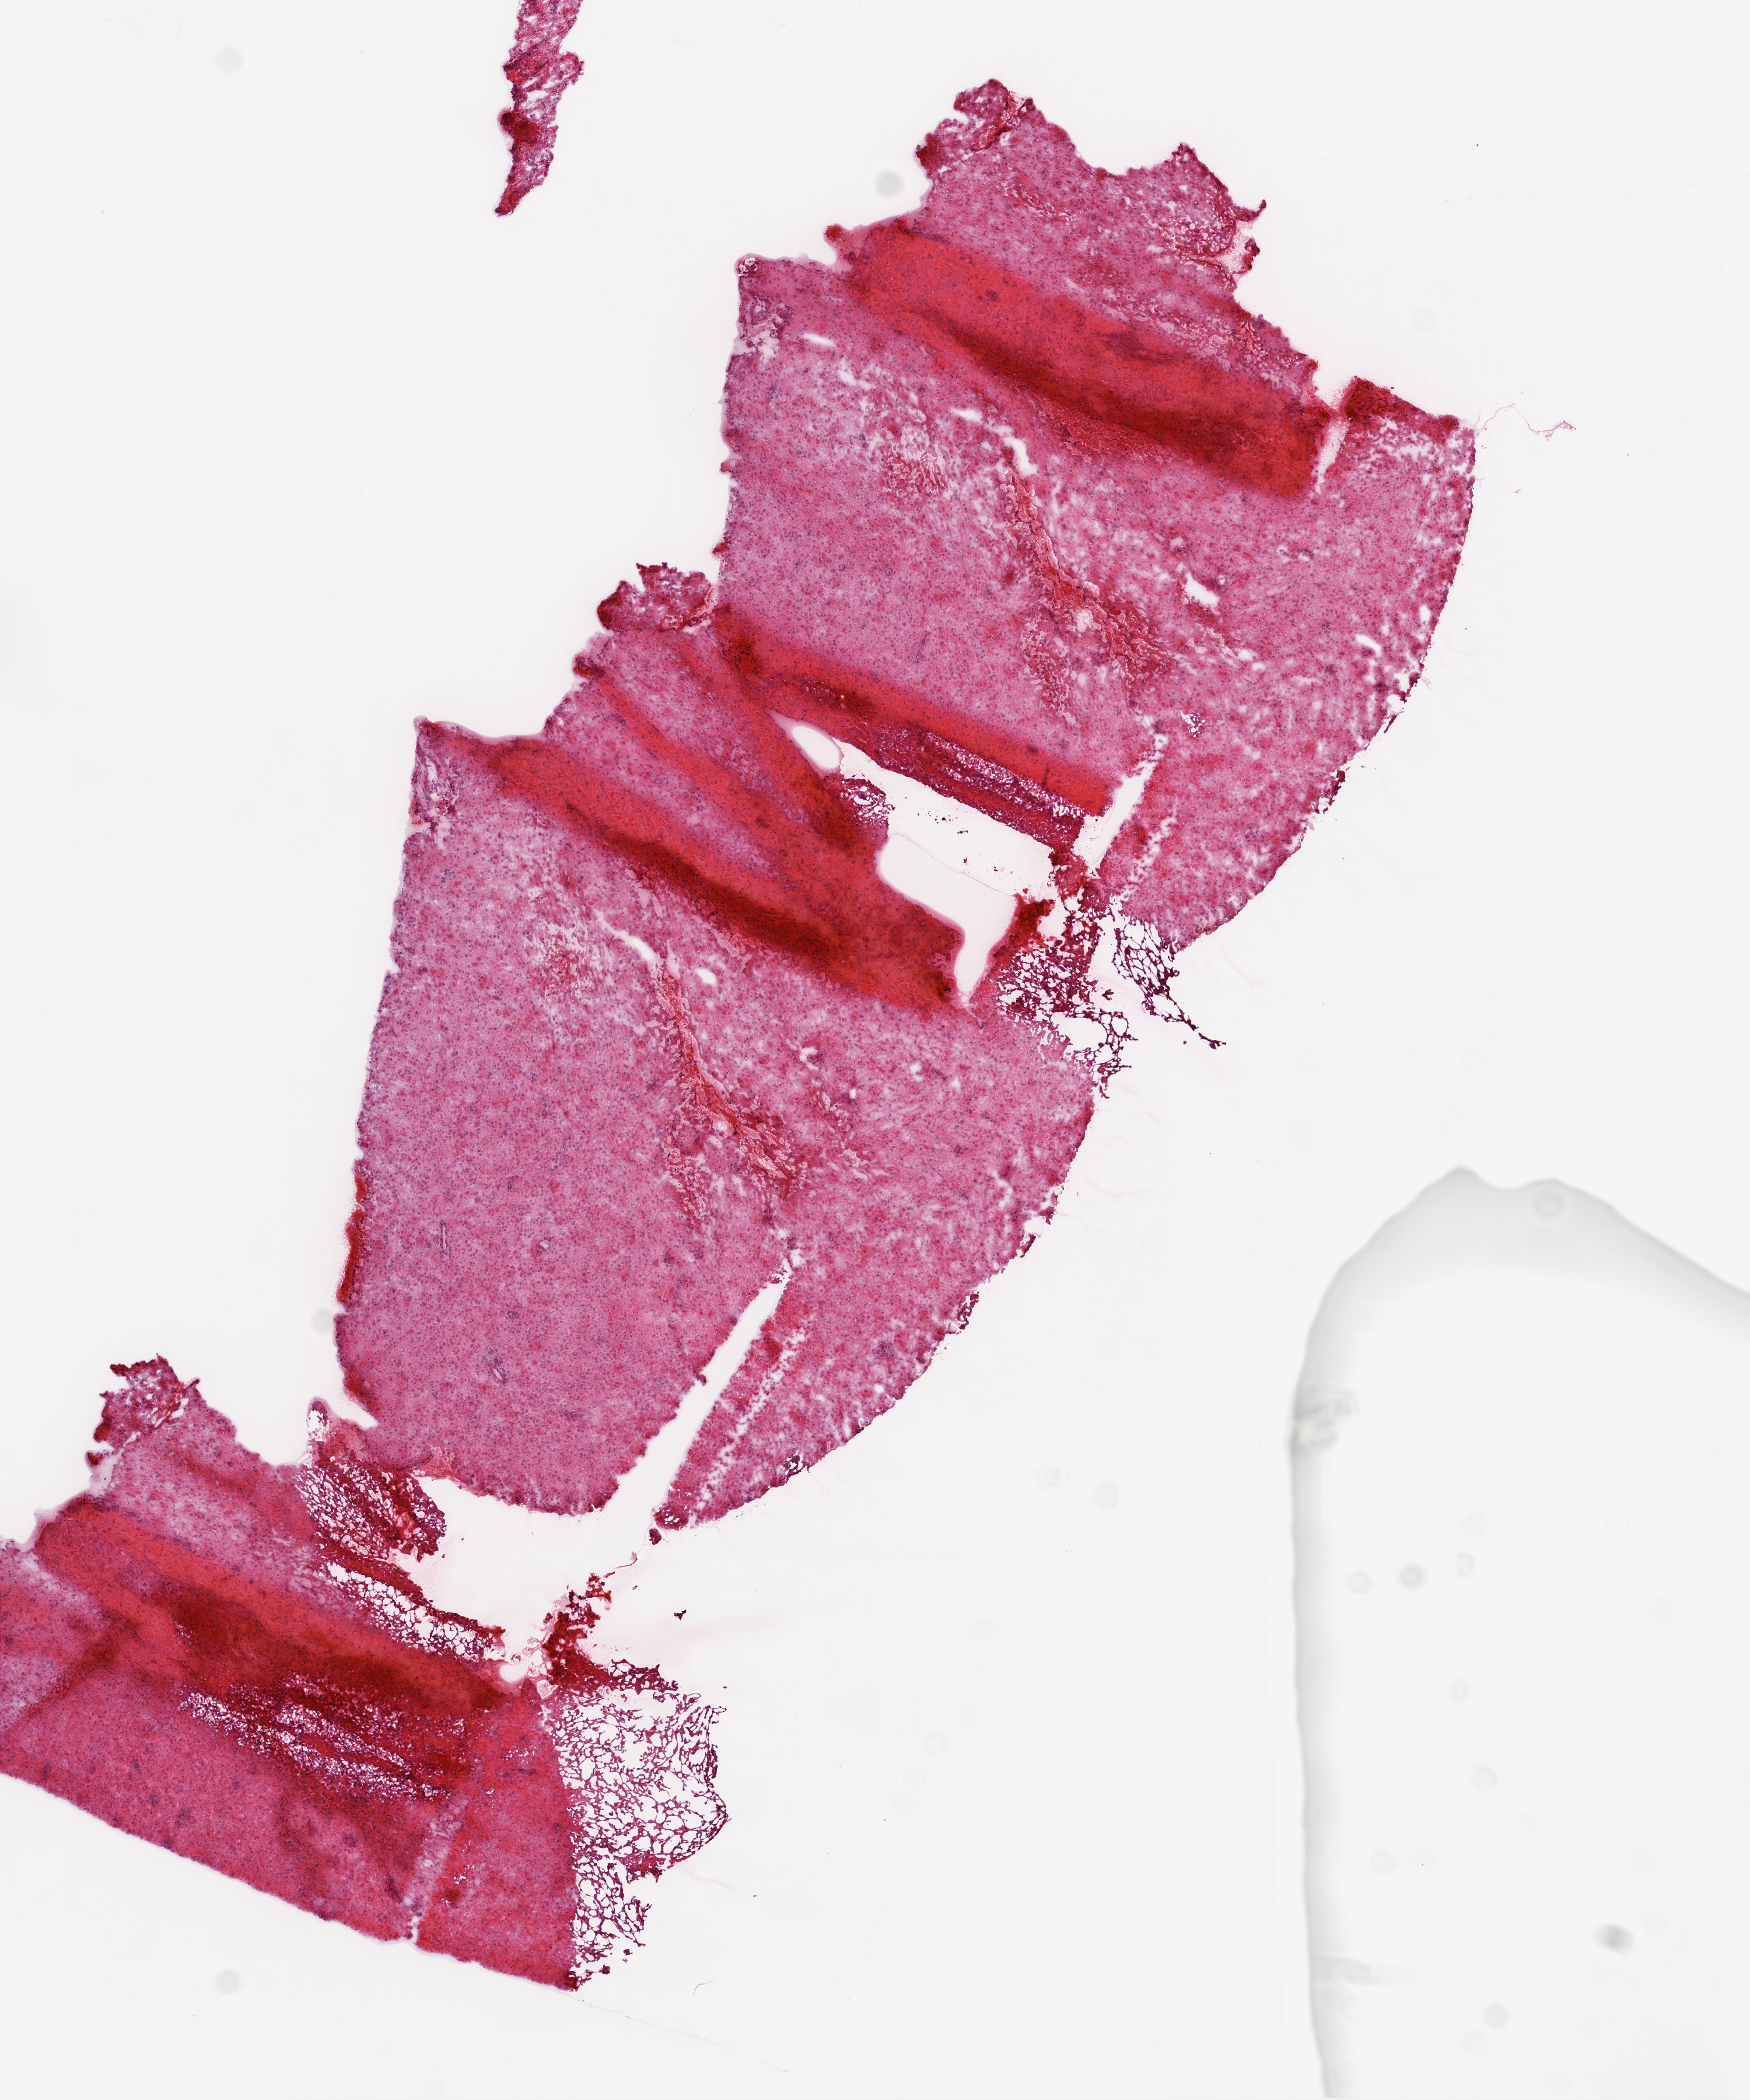
Digitized H&E-stained tissue section (whole slide), low-resolution overview of the scanned area, about 6.0 x 7.2 mm (slide scanned at 20x). Slide review estimates, as recorded: tumour cells 90%, tumour nuclei 95%, normal cells 0%, stromal cells 0%, necrosis 10%.
Specimen: frozen section; sample: primary tumour, brain.